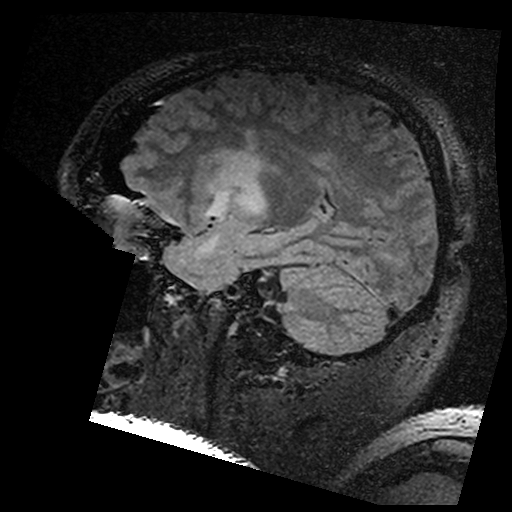
Brain MRI from a brain-tumour surgery series, one sagittal slice; slice 115 of 176 in the series (ordered by position); T2 FLAIR; 1 mm slice thickness; 512 × 512 image matrix. From the clinical record (not read from this slice): histopathology: Astrocytoma; WHO grade: 3; IDH mutation: yes; tumour location: Left Insular.
Annotated regions visible in this slice (outlined manually by an expert reader):
- residual tumour: box from (x=202, y=147) to (x=276, y=200) px